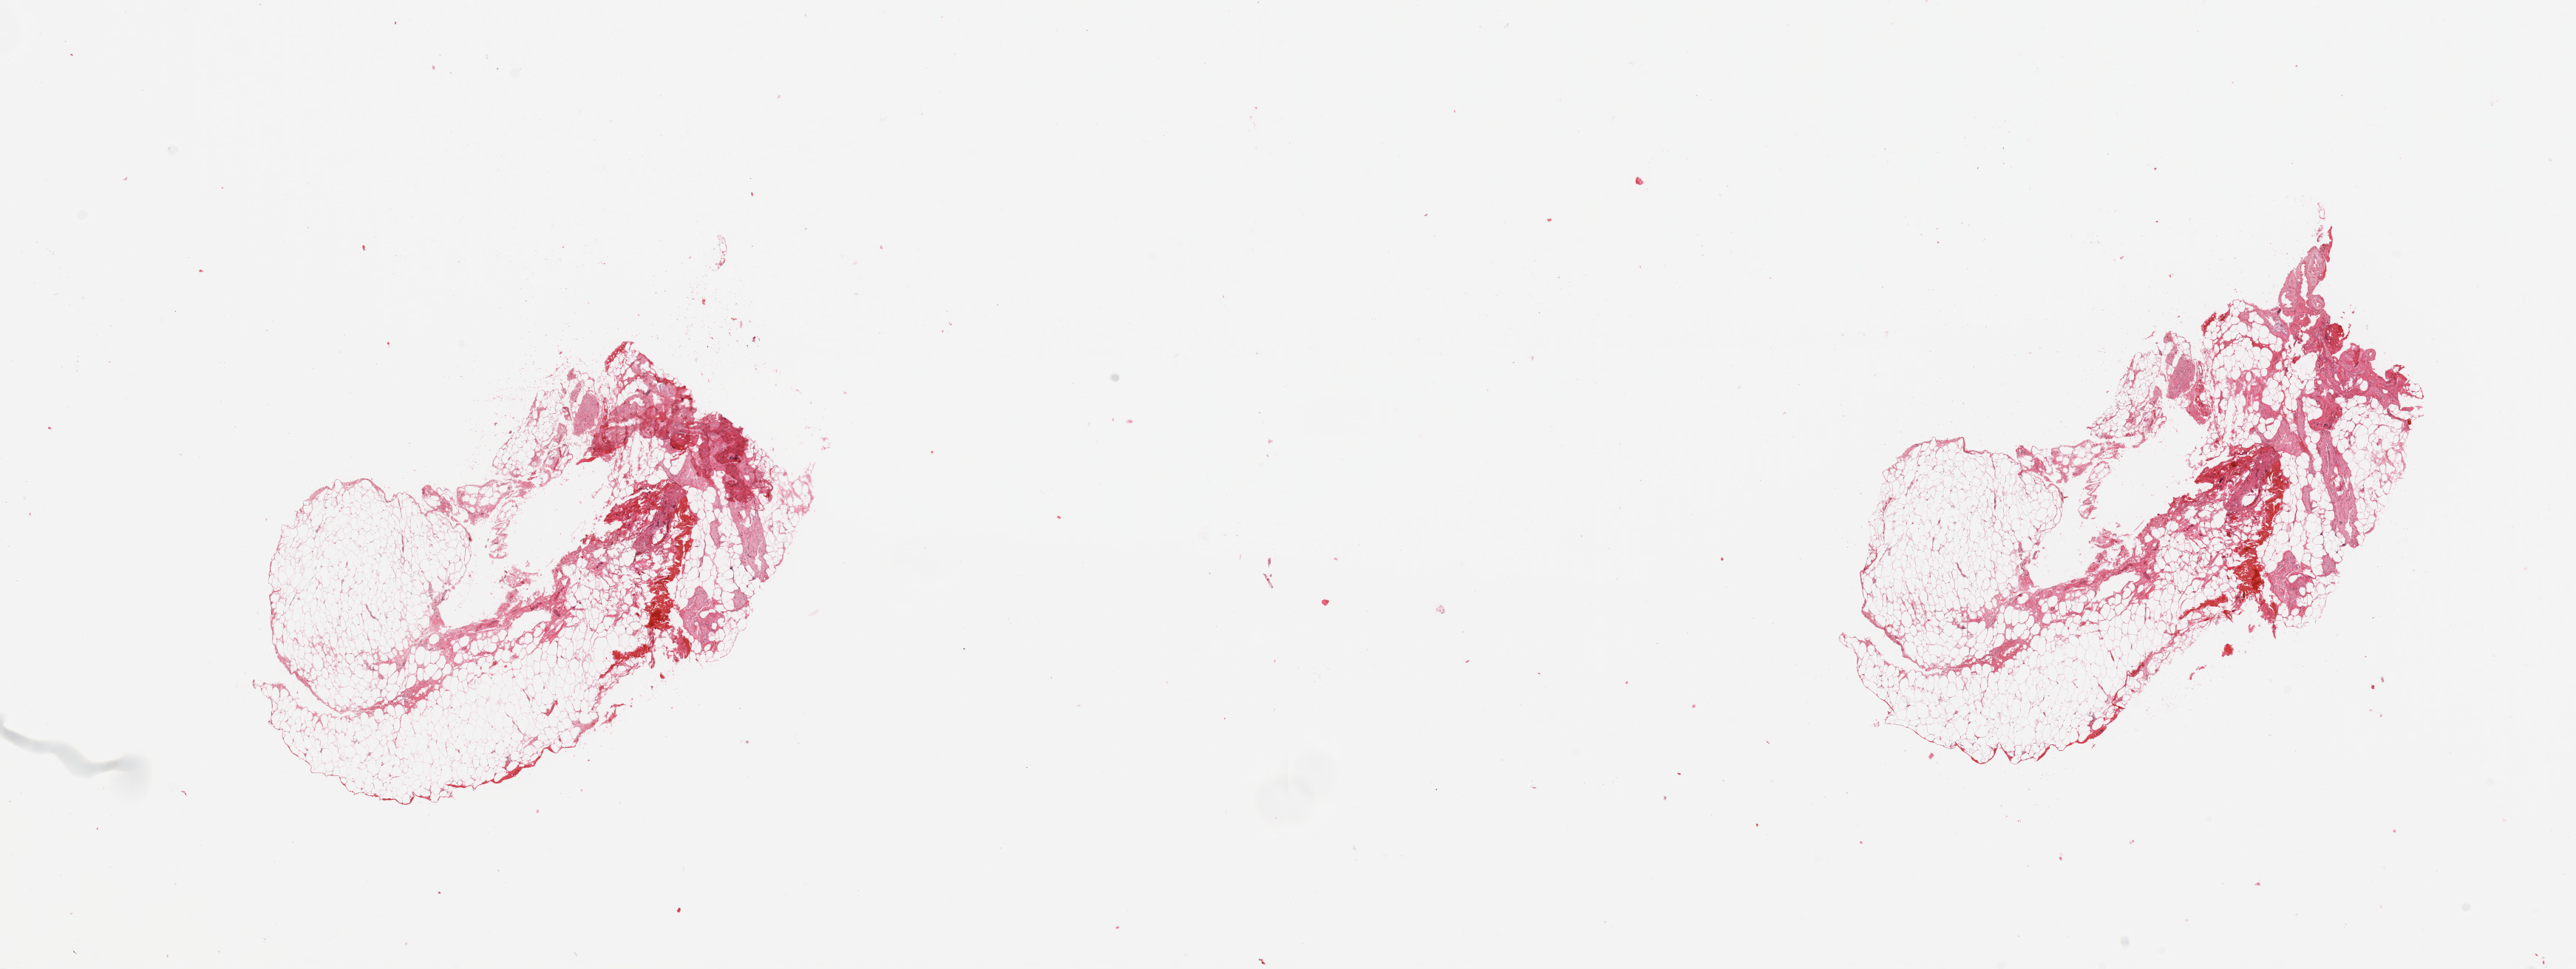
Hematoxylin and eosin (H&E) stained whole-slide image, a low-resolution overview of the entire scanned area, about 27.6 x 10.4 mm. Normal (non-tumour) tissue sample, pancreas. 77-year-old female patient.
This section: normal (non-tumour) tissue from the same patient. Patient diagnosis: Infiltrating duct carcinoma, NOS.